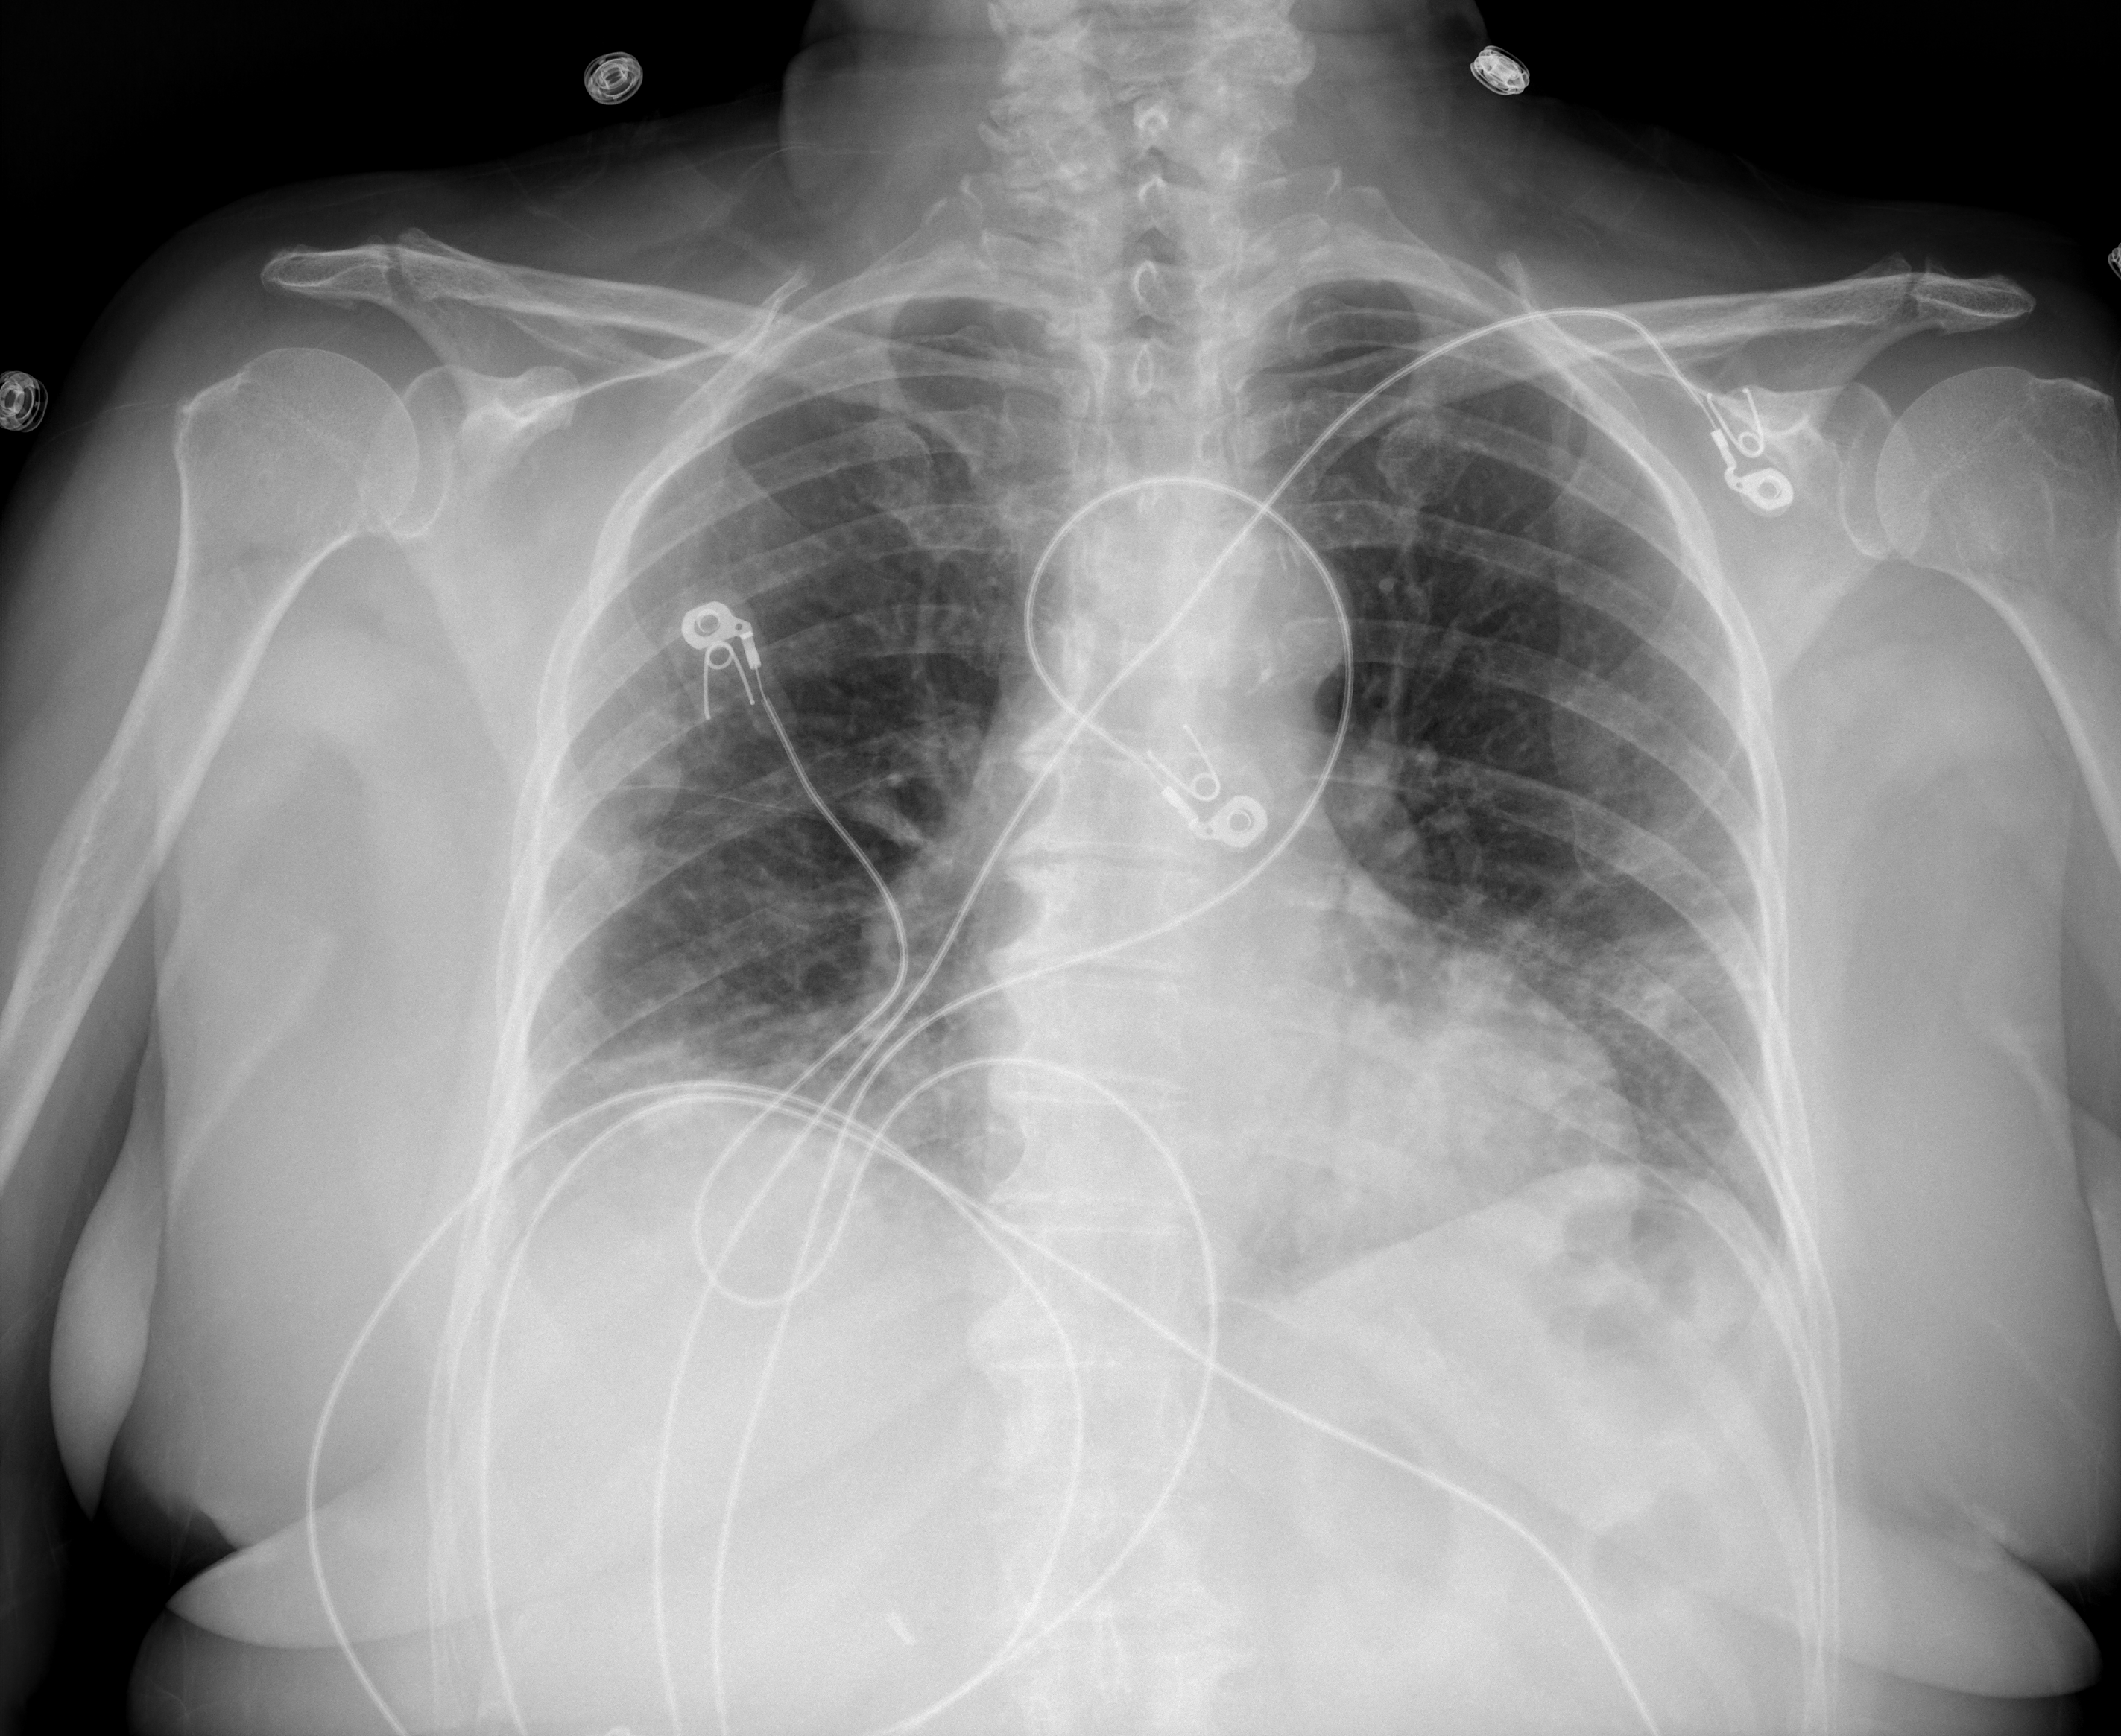
Portable chest radiograph, AP projection. Female patient, age 67 years; COVID-19 (test-positive).
Key findings recorded by the radiologist: Bibasilar airspace opacities.